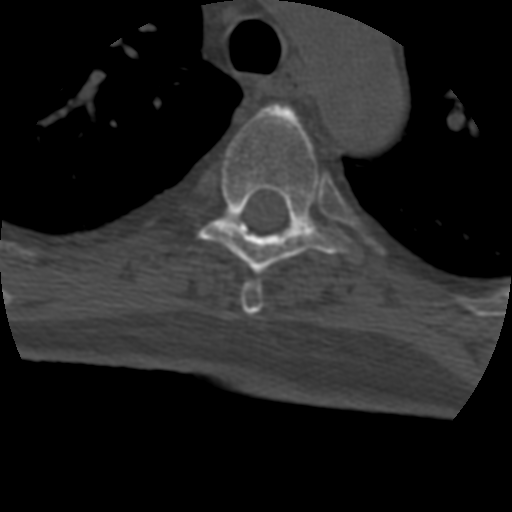
CT including the spine, one axial slice. Position 320 of 399 along the scan axis. Reconstruction kernel STANDARD. 120 kVp. Bone window (W 1800 / L 400 HU). 1.25 mm slice thickness. 512 × 512 image matrix, field of view 160 × 160 mm. Patient age 69 years. Case-level facts recorded for this patient, not image findings: primary cancer: prostate.
Outlined on this slice (semi-automatic segmentation, software-assisted and operator-edited):
- T4 vertebra: box from (x=241, y=282) to (x=263, y=315) px
- T5 vertebra: (x=197, y=104)–(x=358, y=275)